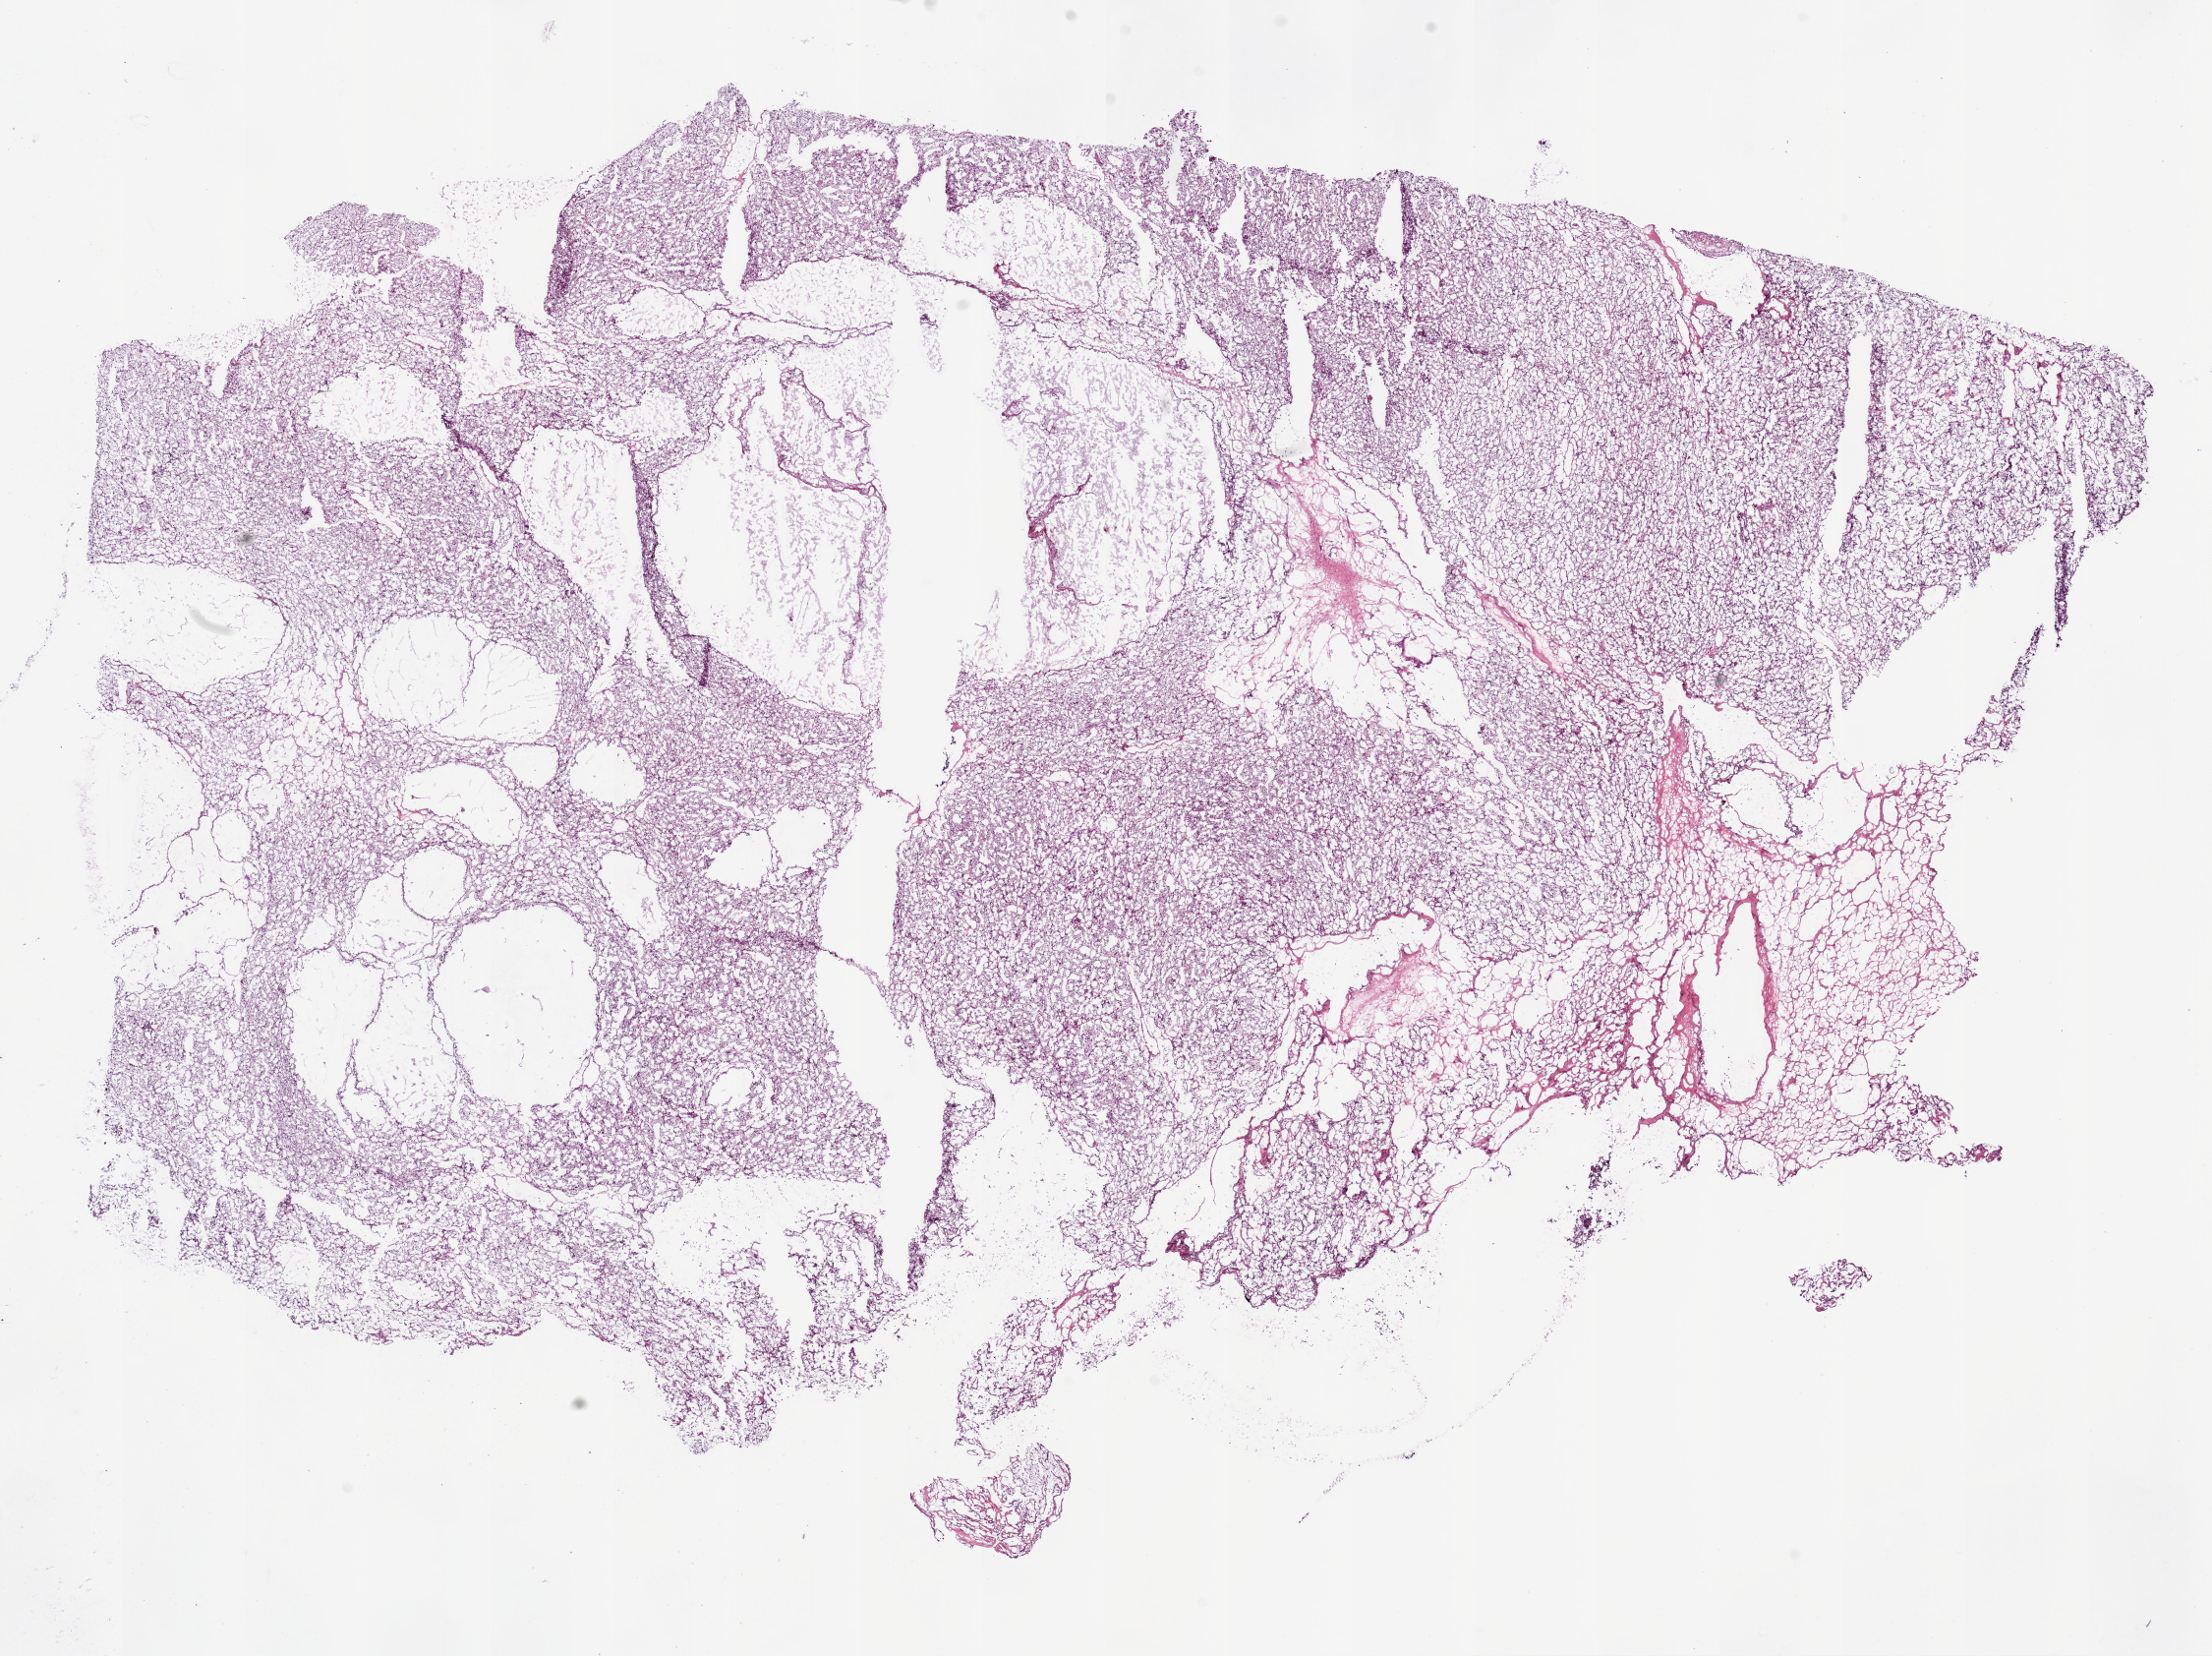
H&E whole-slide image — whole scanned area (about 18.1 x 13.5 mm) shown as a low-resolution overview, frozen section from the bottom of the tissue portion, sample: primary tumour, kidney. Male, age 75 years at initial diagnosis. Histologic grade: G2 (moderately differentiated). Pathologist review of this section (percent, as recorded): tumour cells 95%, tumour nuclei 85%, normal cells 0%, stromal cells 5%, necrosis 0%.
AJCC pathologic stage: I. TNM: T1a NX M0. Diagnosis: Clear cell adenocarcinoma, NOS.